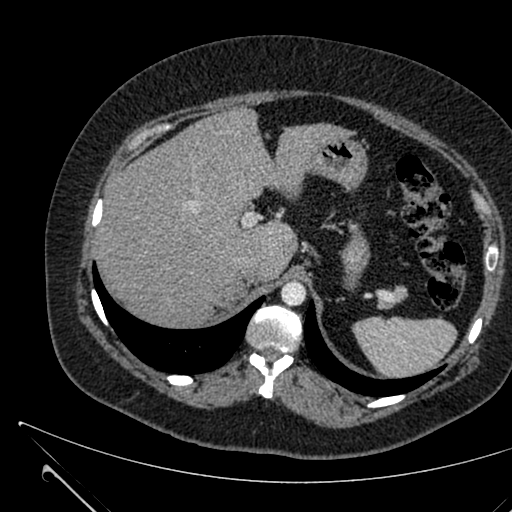
Contrast-enhanced abdominal CT, one axial slice. Slice 488 of 731 in the series (ordered by position). 120 kVp. Intravenous contrast given. Soft-tissue window (W 400 / L 40 HU). 1 mm slice thickness. 512 × 512 image matrix, field of view 376 × 376 mm. Patient: female, 36 years. From the clinical record (not read from this slice): diagnosis: adrenocortical carcinoma; tumour side: right adrenal; tumour size at pathology: 10 cm.
Outlined on this slice (semi-automatic segmentation, software-assisted and operator-edited):
- mass: bounding box (x1, y1, x2, y2) in pixels: (221, 277, 244, 306)